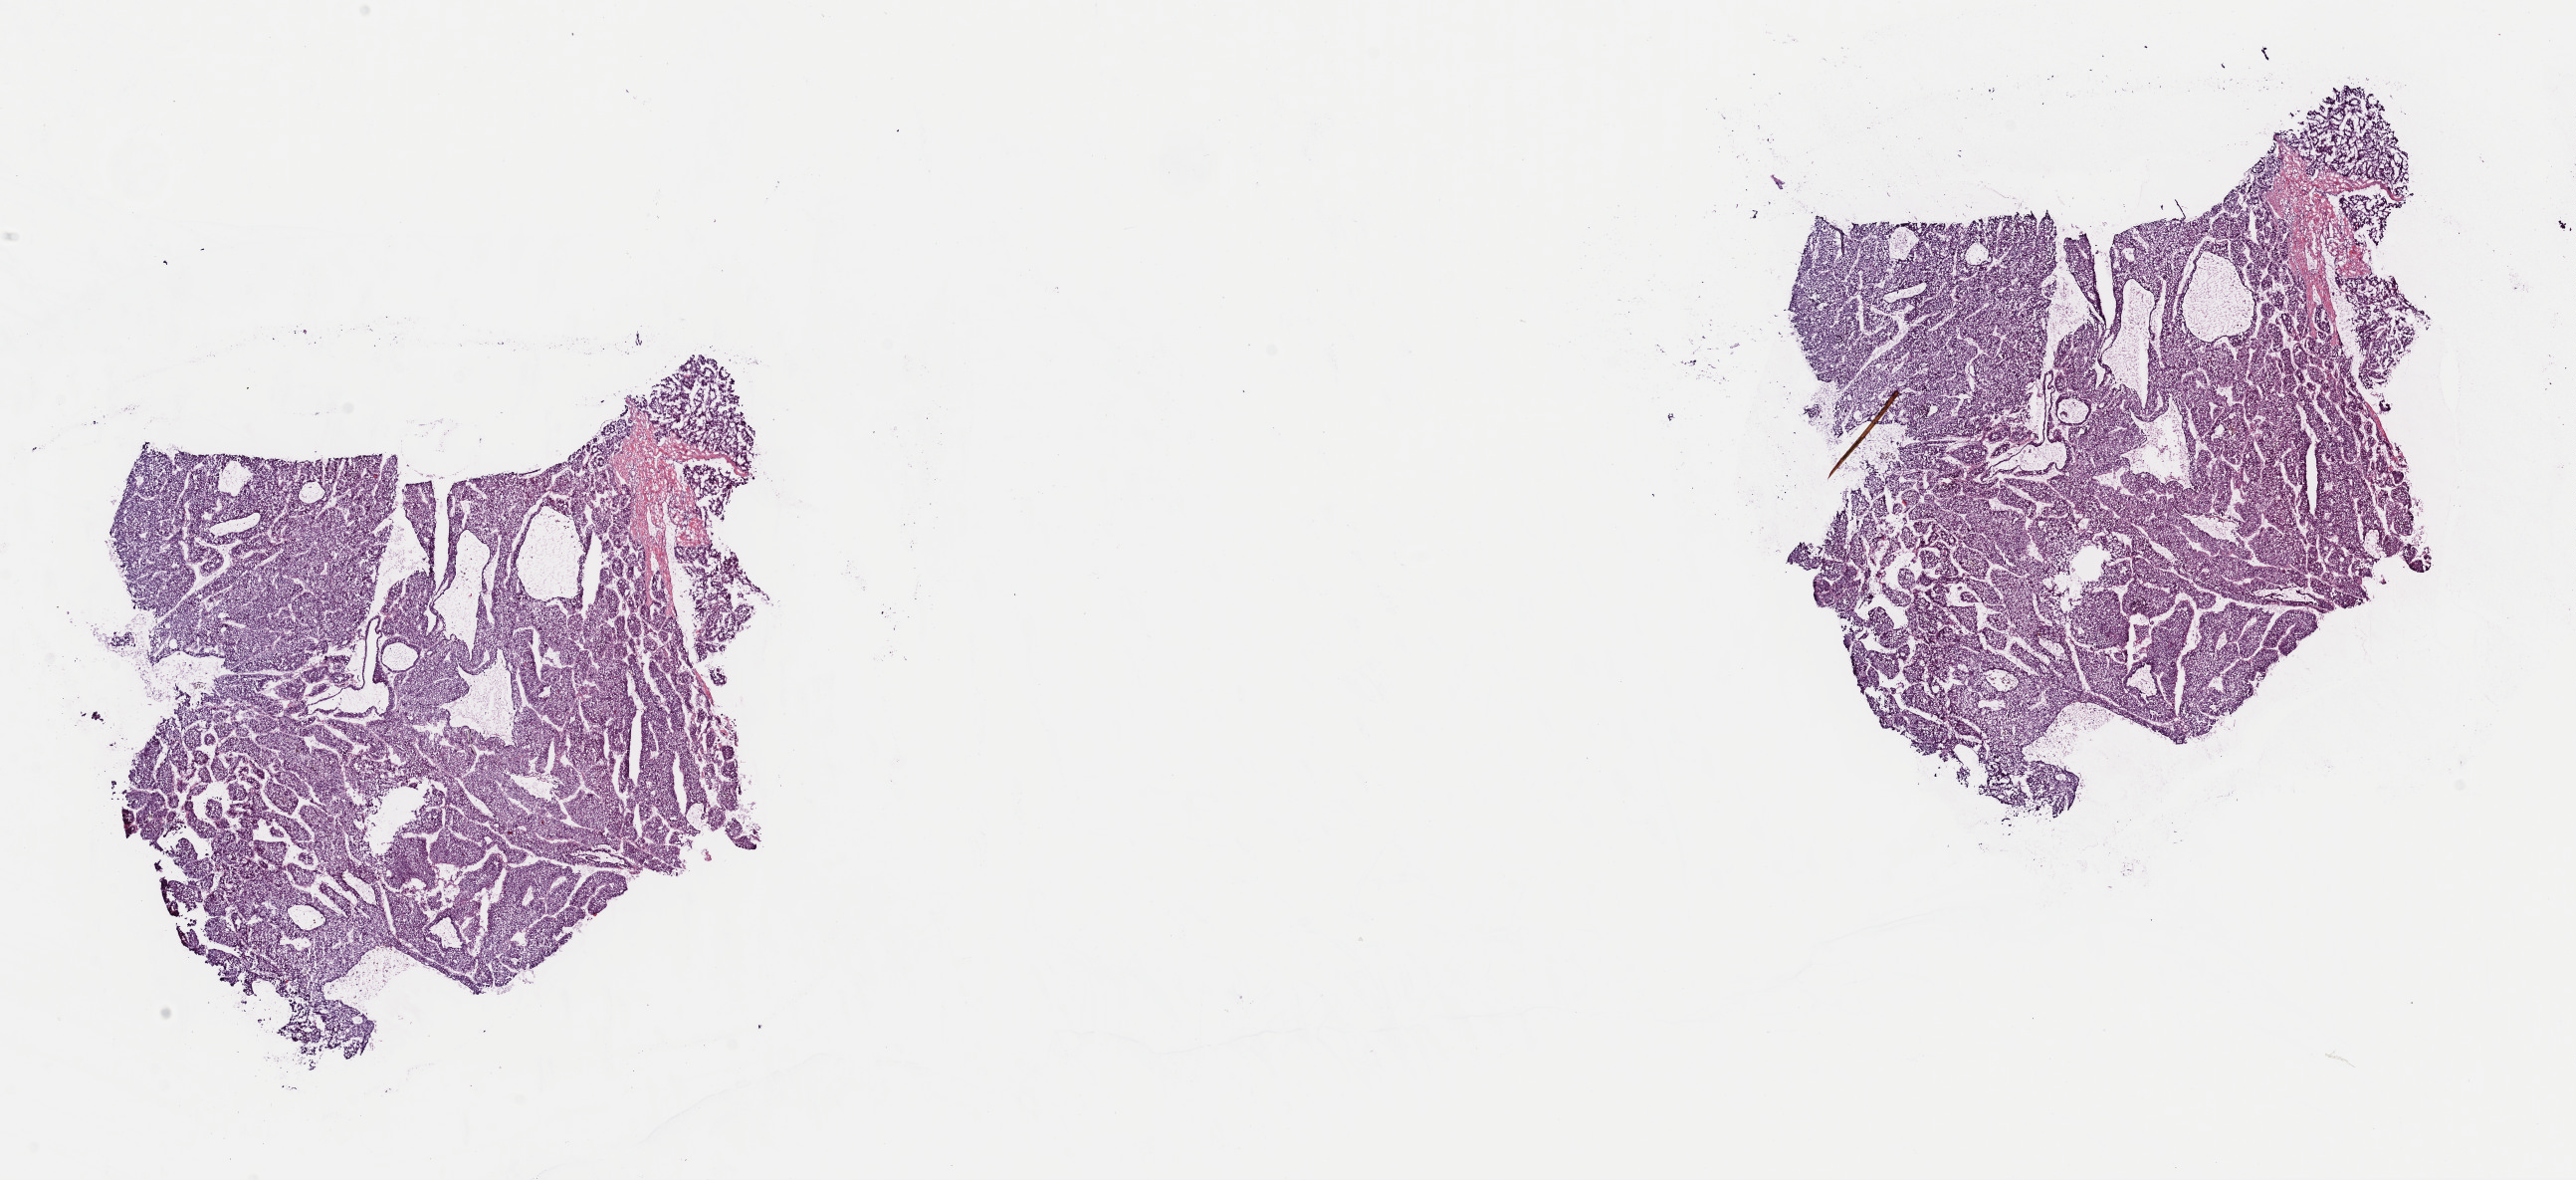
Whole-slide histology image, H&E, a low-resolution overview of the entire scanned area, about 20.4 x 9.4 mm (from a 40x scan). Frozen section. Liver, primary tumour sample. Patient: male, age at initial diagnosis 63 years. Pathologist review of this section (percent, as recorded): tumour cells 87%, tumour nuclei 90%.
Pathologic diagnosis: Hepatocellular carcinoma, NOS.